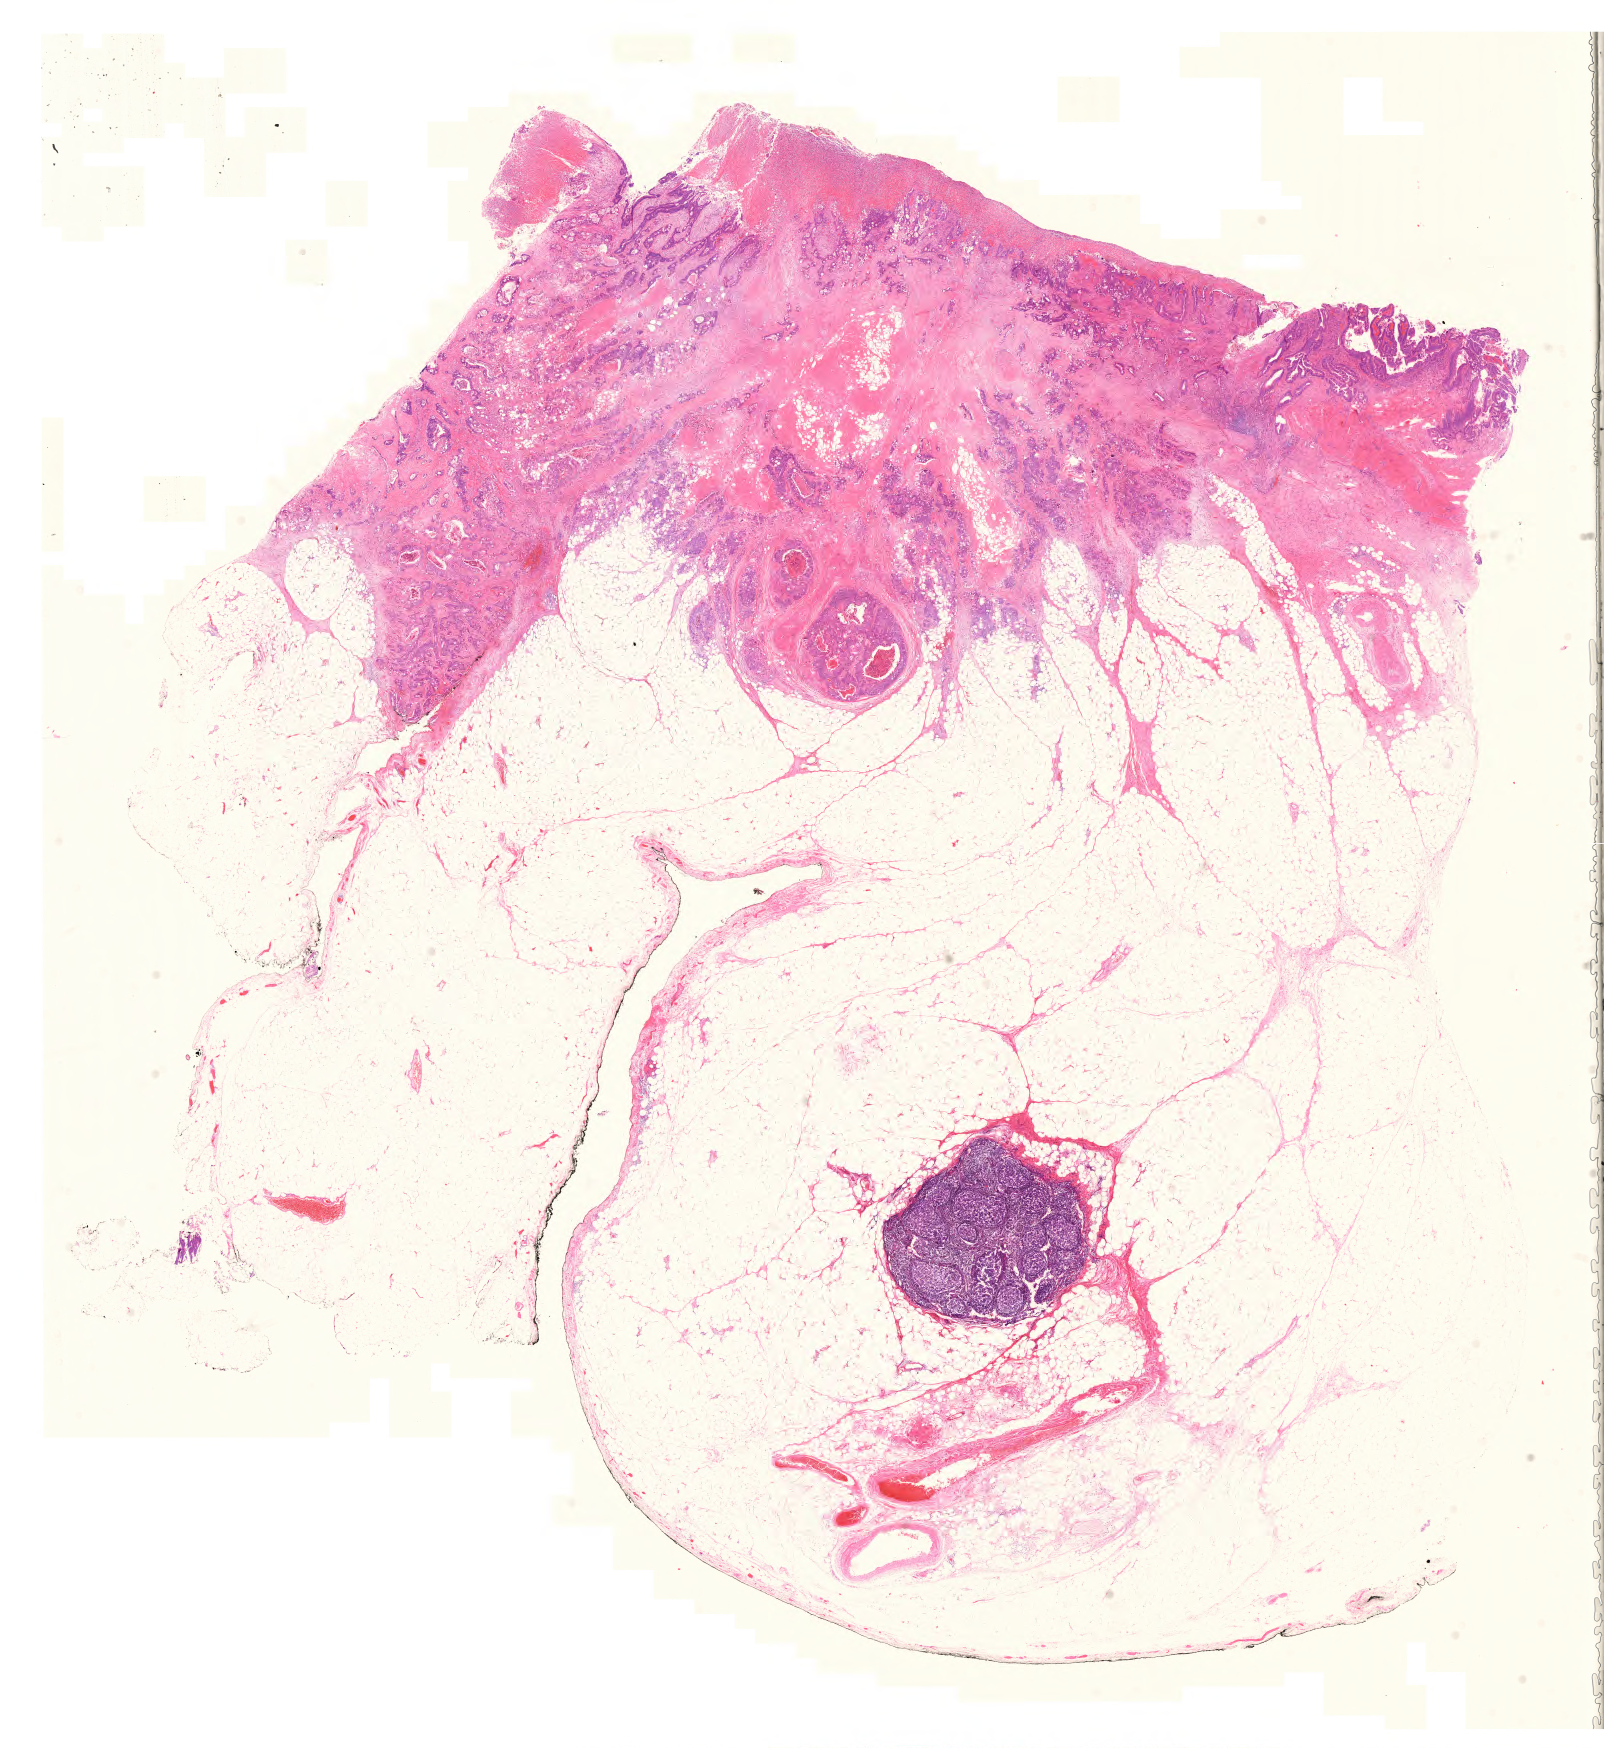
Whole-slide histology image, H&E-stained — whole scanned area (about 23.9 x 26.0 mm) shown as a low-resolution overview, FFPE section, primary tumour sample from the uterus. Female patient; age at initial diagnosis 54 years. Histologic grade: G1 (well differentiated).
Diagnosis: Endometrioid adenocarcinoma, NOS. FIGO stage: I.